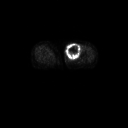
FDG PET of an extremity soft-tissue mass (from a PET/CT study), one axial slice; position 36 of 91 along the scan axis; 128 × 128 image matrix. Patient: female, 74 years. Case-level facts recorded for this patient, not image findings: histological type: pleomorphic leiomyosarcoma; grade: high; site of the primary tumour: left thigh.
Outlined on this slice (expert contour drawn on MRI and transferred to this co-registered scan by the dataset authors):
- gross tumour volume including surrounding oedema: bounding box <65,42,82,61> (left, top, right, bottom; pixels)
- gross tumour volume (mass): <65,42,81,60>